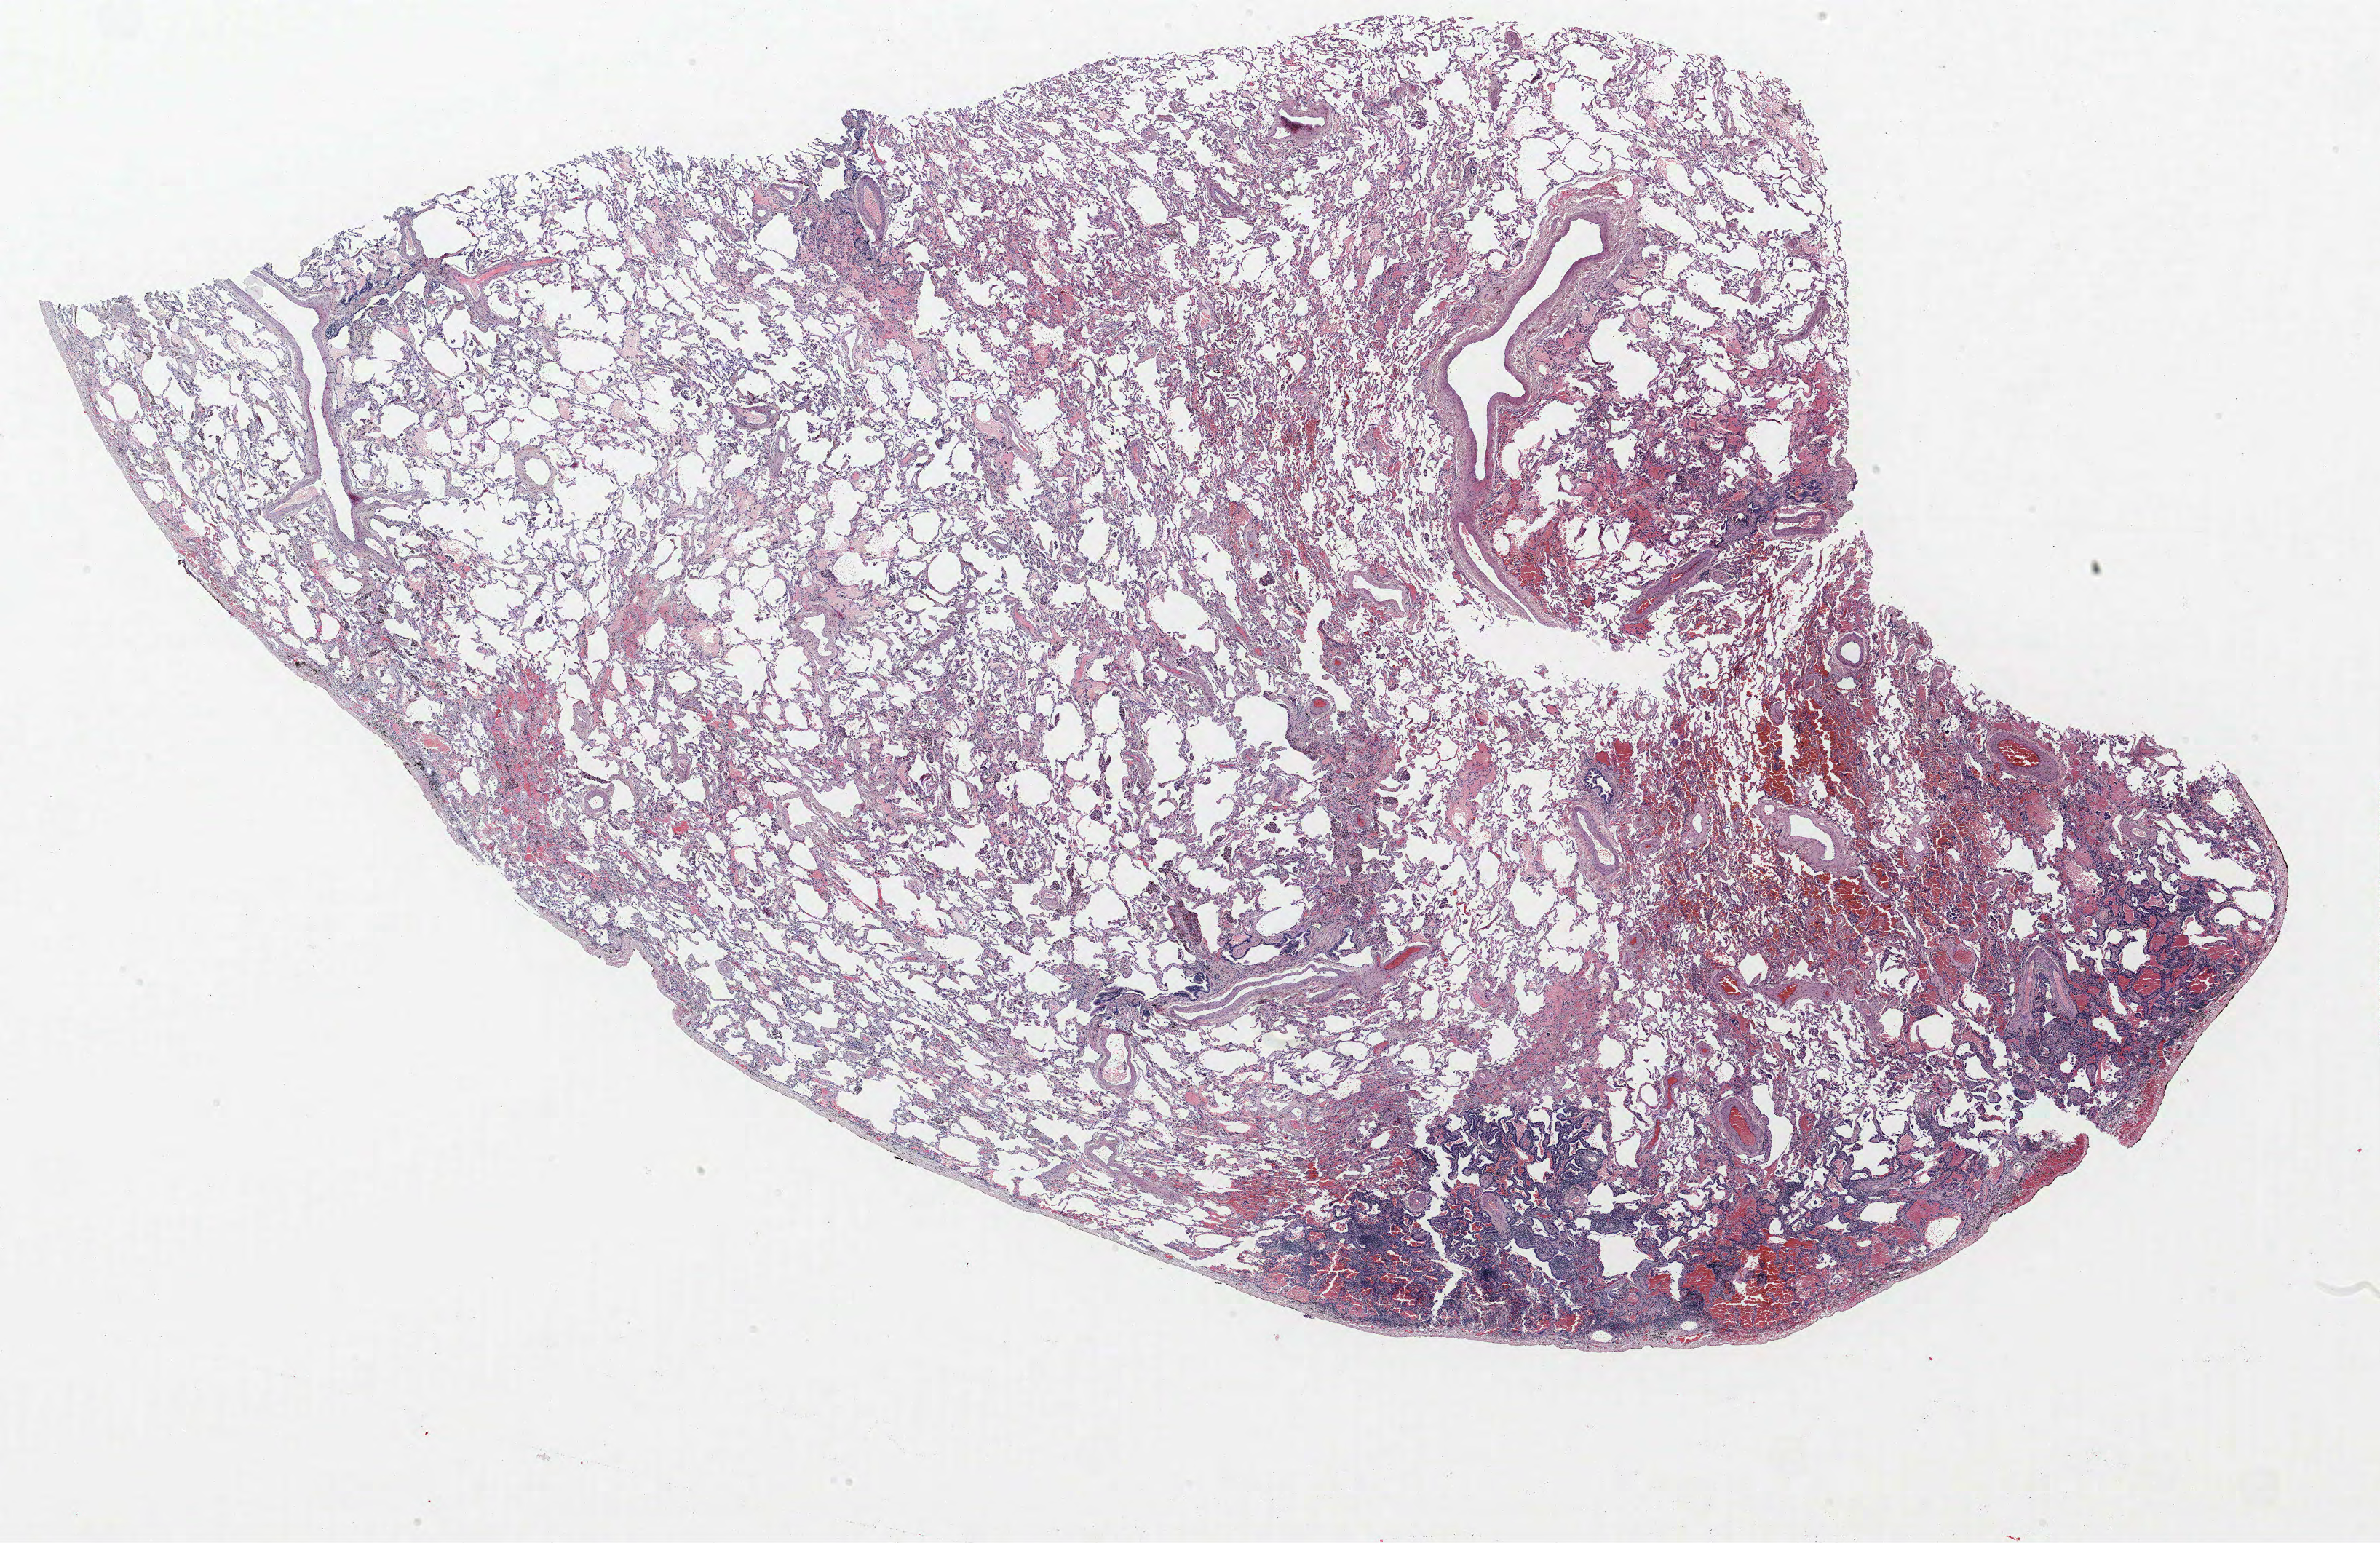
Whole-slide histology image, H&E-stained, low-resolution overview of the scanned area, about 26.2 x 17.0 mm. FFPE section. Lung tissue. Male patient, aged 60 at enrolment. Current smoker at enrolment. Grade: well differentiated (G1).
Participant's lung-cancer diagnosis: Bronchiolo-alveolar adenocarcinoma, NOS (ICD-O-3 8250/3). Tumour size (pathology): 27 mm. Stage (AJCC 6th edition): IA. Primary tumour location (clinical record): left upper lobe.